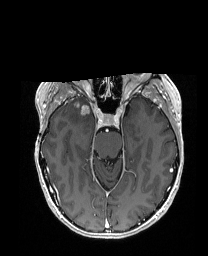
Brain MRI from a brain-tumour surgery series, one axial slice; slice 115 of 192 in the series (ordered by position); T1-weighted post-contrast; 1 mm slice thickness; 208 × 256 image matrix, field of view 203 × 250 mm. From the clinical record (not read from this slice): histopathology: Metastatic Carcinoma from Breast primary; tumour location: Right Frontal.
Structures marked on this image (manually delineated by an expert):
- tumour: bounding box <79,102,95,113> (left, top, right, bottom; pixels)